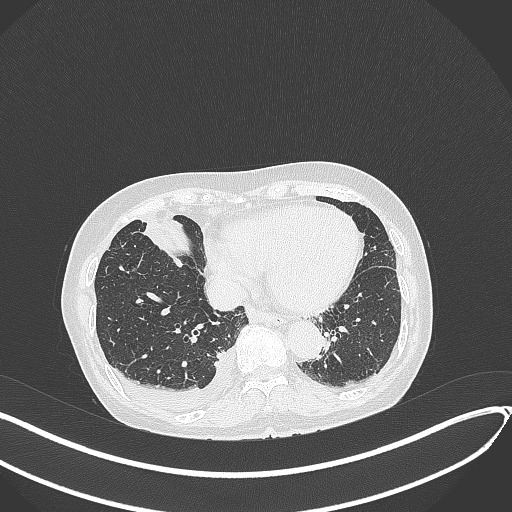
Chest CT, one axial slice. Position 114 of 418 along the scan axis. Reconstruction kernel B70f. 120 kVp. Lung window (W 1500 / L -600 HU). 1 mm slice thickness. 512 × 512 image matrix, field of view 400 × 400 mm. Female patient, age 75 years. Case-level facts recorded for this patient, not image findings: clinical TNM (as recorded): T2a N3 M0.
Structures marked on this image (rectangle marked by the reading radiologist):
- lung tumour (recorded histology: adenocarcinoma): bounding box [x1, y1, x2, y2] px = [142, 214, 192, 259]